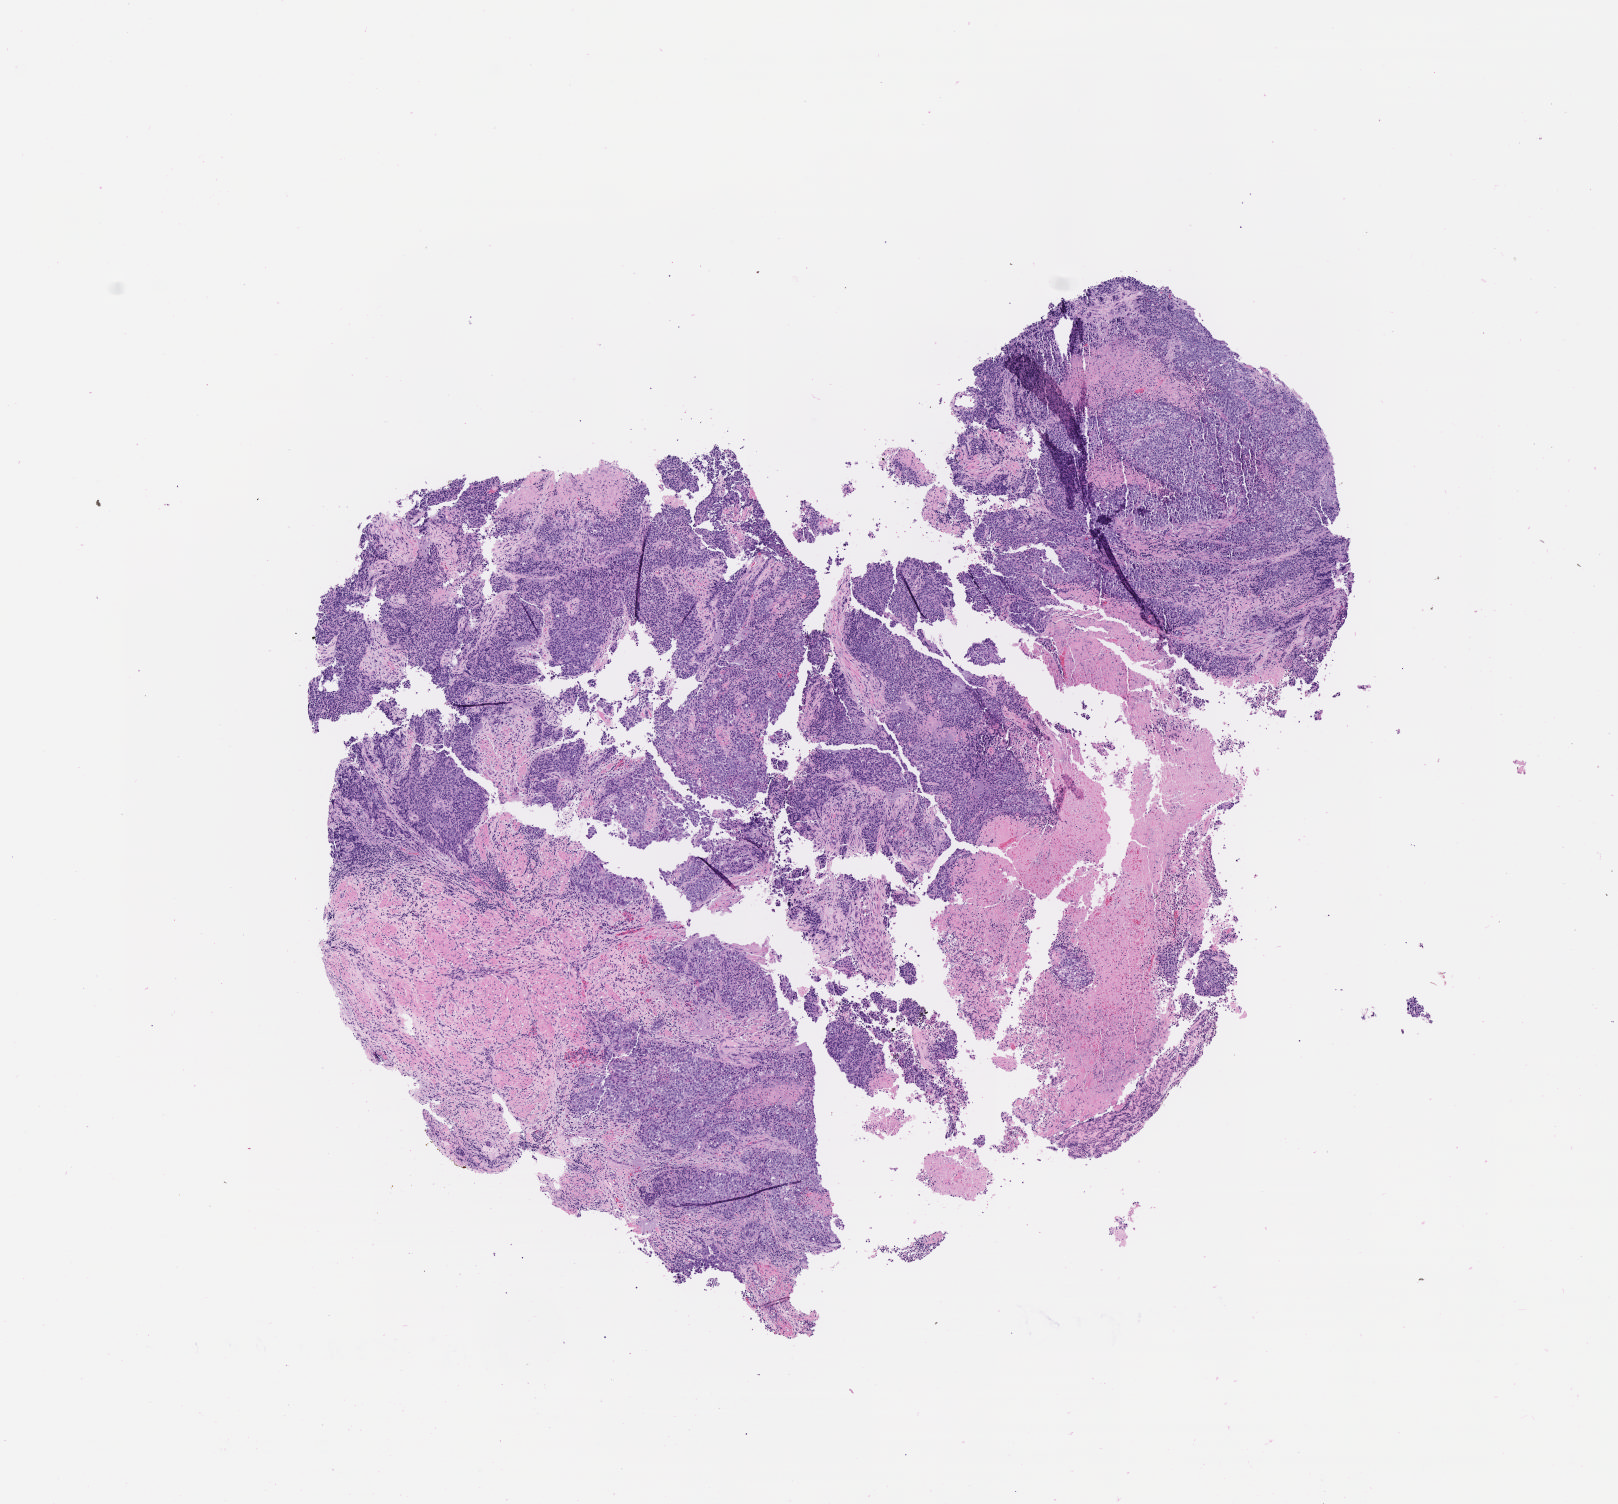
Digitized haematoxylin and eosin-stained section — shown as a low-resolution overview of the whole scanned area (about 6.5 x 6.1 mm); specimen: tumor tissue; anatomic site: cervix. Patient female; age 54 years.
- histologic diagnosis: Squamous cell carcinoma, large cell, nonkeratinizing, NOS